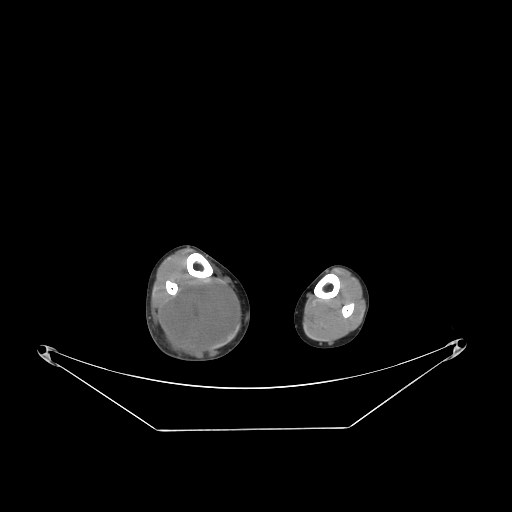
CT of an extremity soft-tissue mass (from a PET/CT study), one axial slice; position 76 of 267 along the scan axis; reconstruction kernel STANDARD; soft-tissue window (W 400 / L 40 HU); 512 × 512 image matrix, field of view 500 × 500 mm. Male patient. Case-level facts recorded for this patient, not image findings: histological type: liposarcoma - round cell; grade: high; site of the primary tumour: right calf.
Annotated regions visible in this slice (expert contour drawn on MRI and transferred to this co-registered scan by the dataset authors):
- gross tumour volume (mass): box from (x=162, y=279) to (x=239, y=362) px